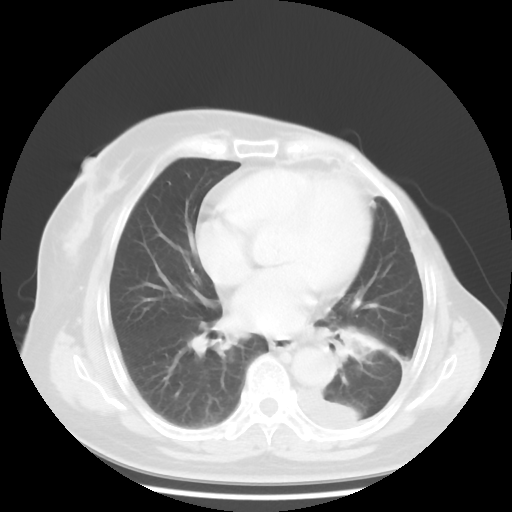
Chest CT, one axial slice; reconstruction kernel STANDARD; lung window (W 1500 / L -600 HU); 5 mm slice thickness; 512 × 512 image matrix, field of view 360 × 360 mm. Female patient, age 63 years. From the clinical record (not read from this slice): clinical TNM (as recorded): T2 N0 M1.
Outlined on this slice (bounding box drawn by a radiologist):
- lung tumour (recorded histology: adenocarcinoma): box from (x=331, y=322) to (x=395, y=374) px